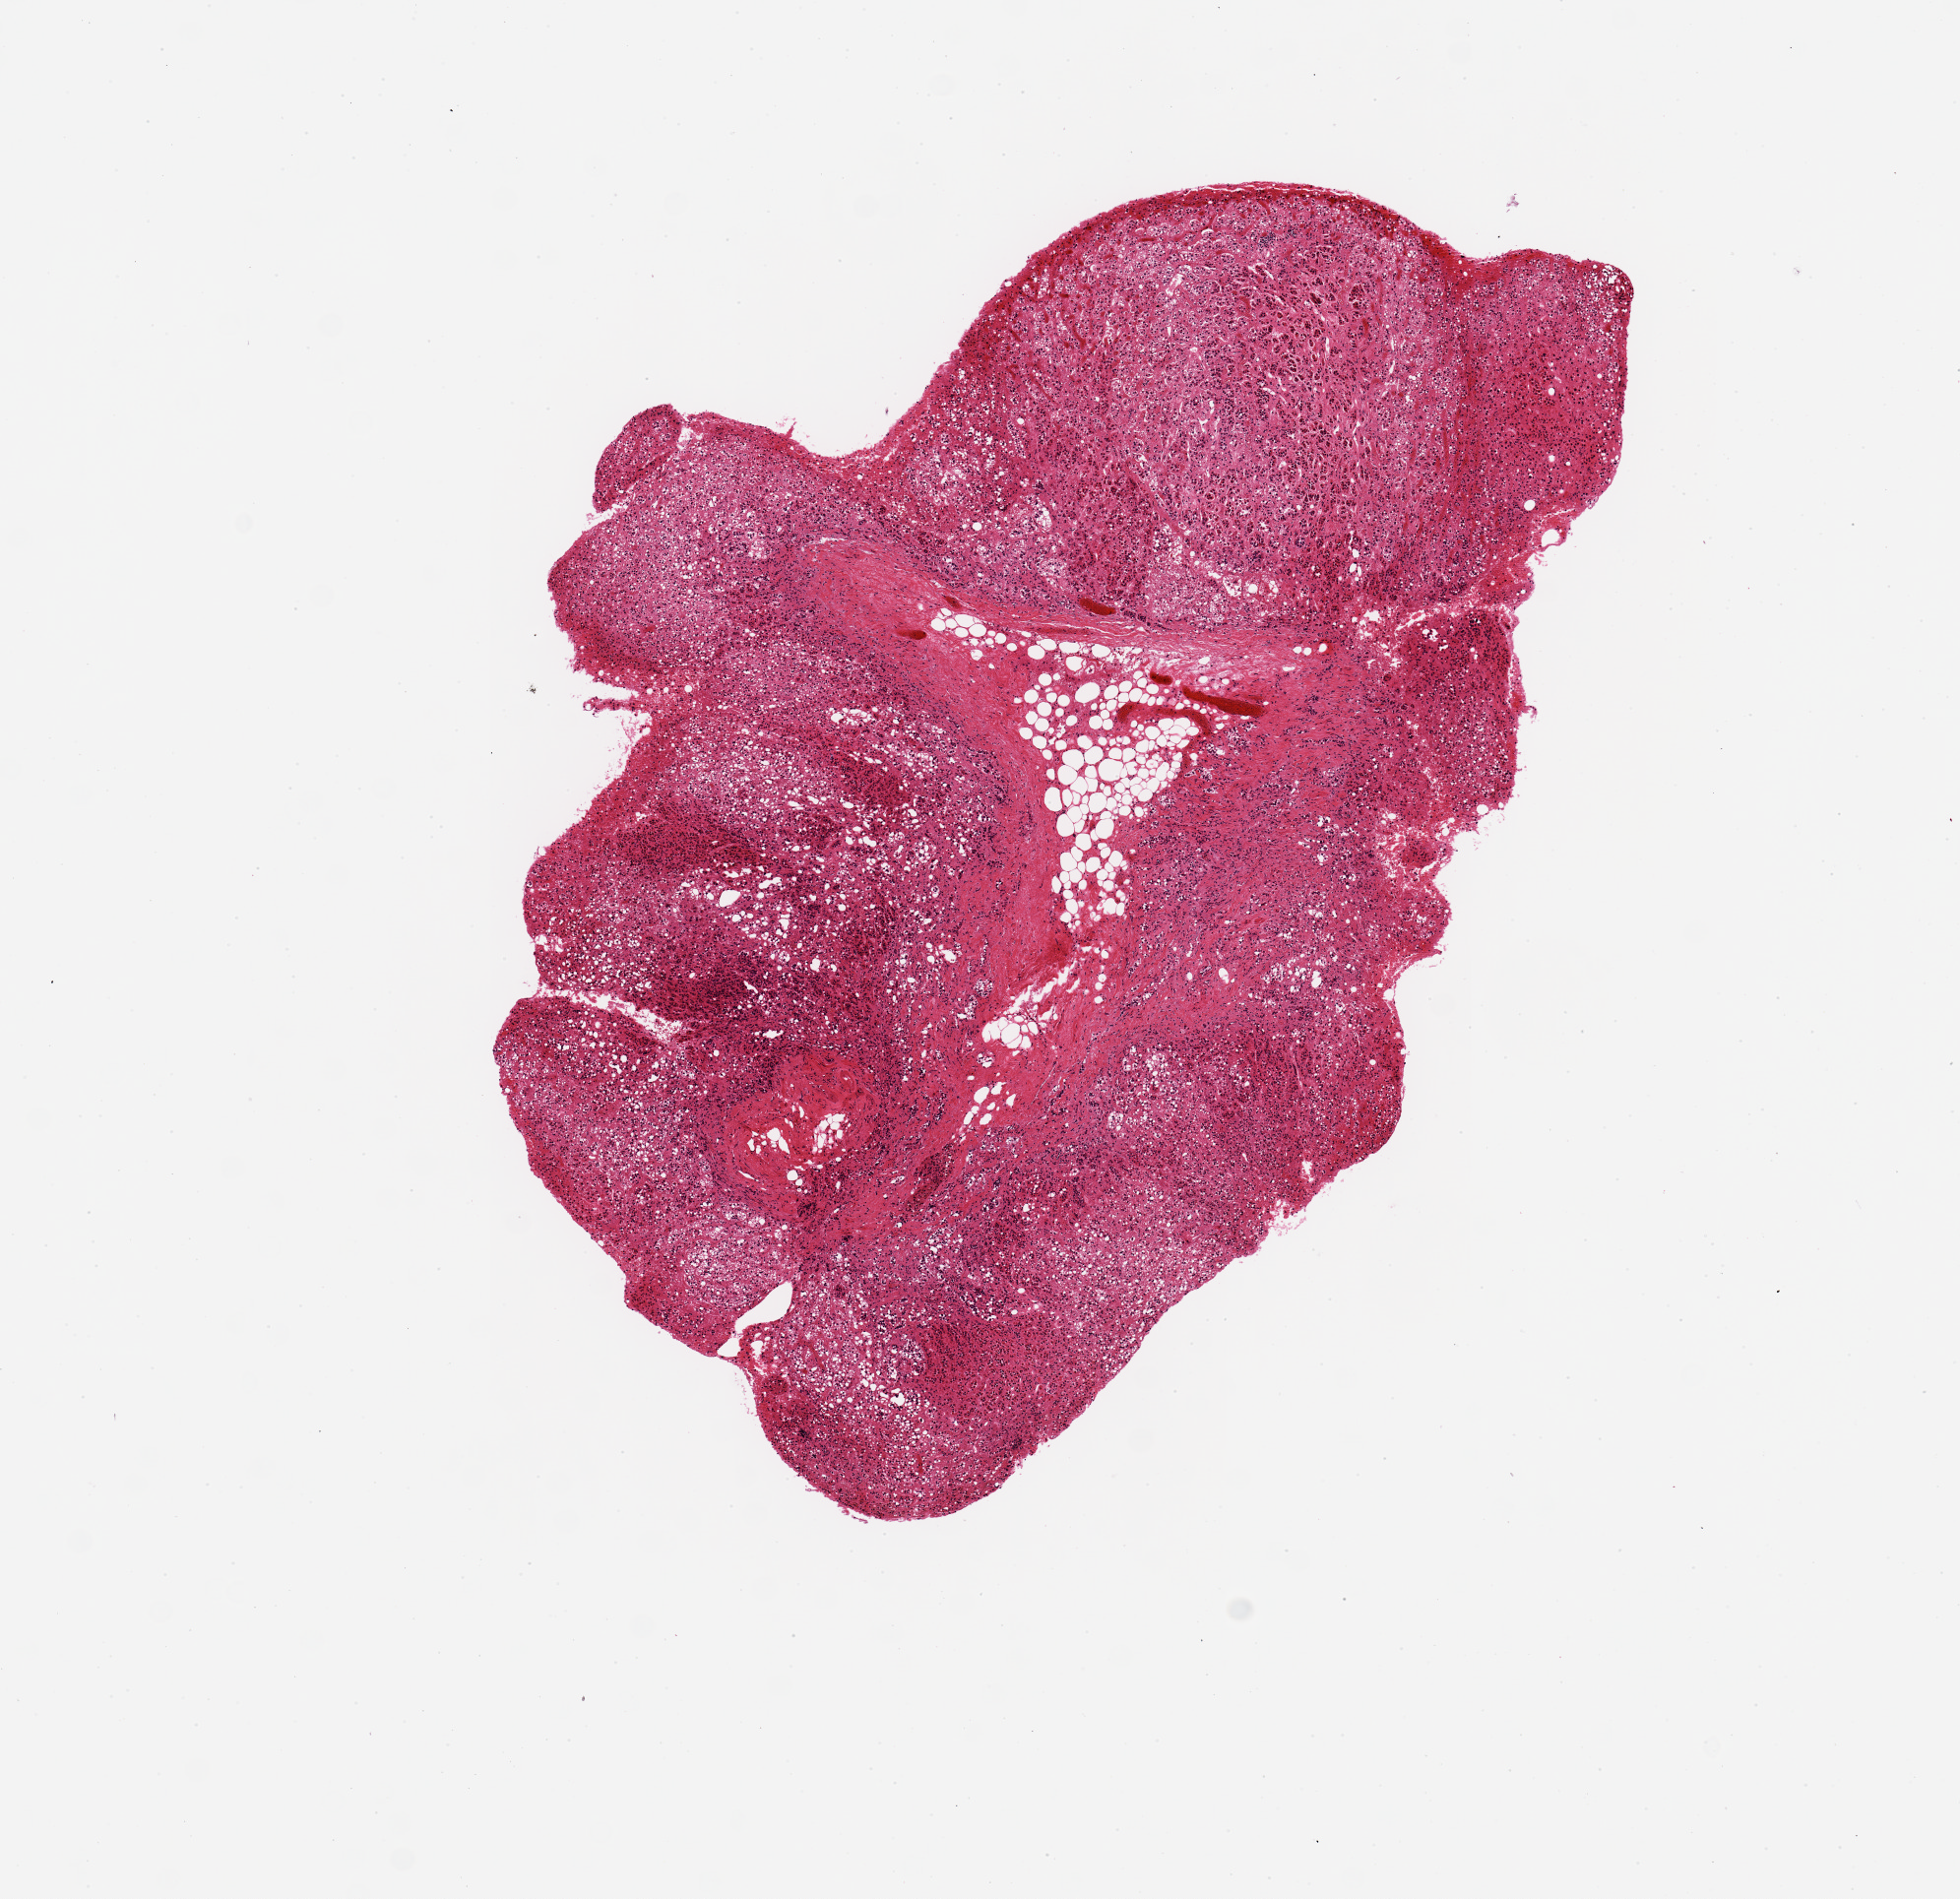
H&E whole-slide image — low-resolution overview of the scanned area, about 7.9 x 7.6 mm (acquisition: 20x scan), PAXgene-fixed paraffin-embedded (PFPE) section, section of adrenal gland (target tissue), donor tissue sample.
Pathologist's review note for this sample: 5x4 mm; cortex; 5% fat.